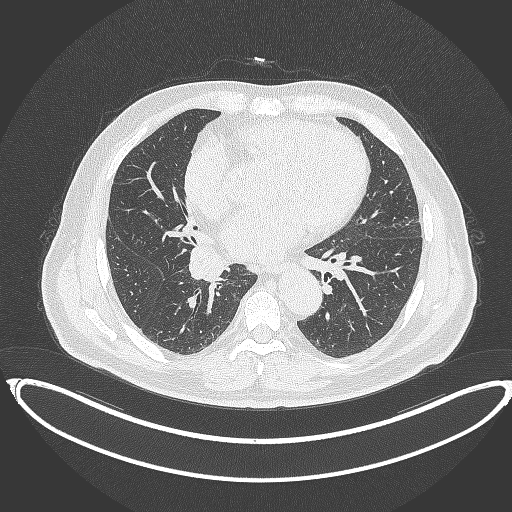
Chest CT, one axial slice; position 189 of 387 along the scan axis; reconstruction kernel B70f; lung window (W 1500 / L -600 HU); 1 mm slice thickness; 512 × 512 image matrix. Patient: male, 61 years. From the clinical record (not read from this slice): clinical TNM (as recorded): T1b N1 M0.
Structures marked on this image (rectangle marked by the reading radiologist):
- lung tumour (recorded histology: squamous cell carcinoma): bounding box <187,243,229,280> (left, top, right, bottom; pixels)